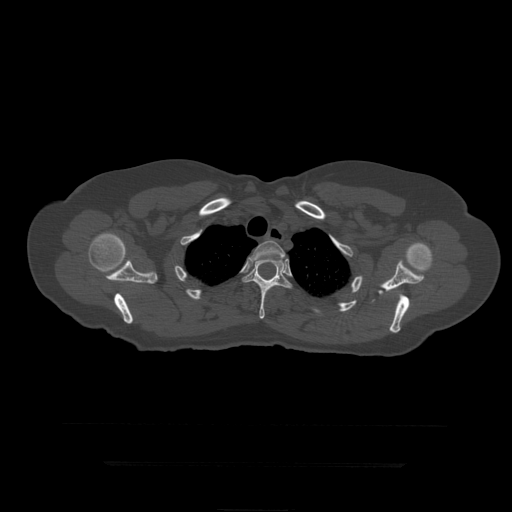
CT including the spine, one axial slice; slice 353 of 399 in the series (ordered by position); reconstruction kernel STANDARD; bone window (W 1800 / L 400 HU); 1.25 mm slice thickness; 512 × 512 image matrix. Patient age 41 years. From the clinical record (not read from this slice): primary cancer: breast.
Annotated regions visible in this slice (semi-automatic segmentation, software-assisted and operator-edited):
- T3 vertebra: box from (x=251, y=241) to (x=286, y=260) px
- T4 vertebra: (x=242, y=256)–(x=293, y=319)